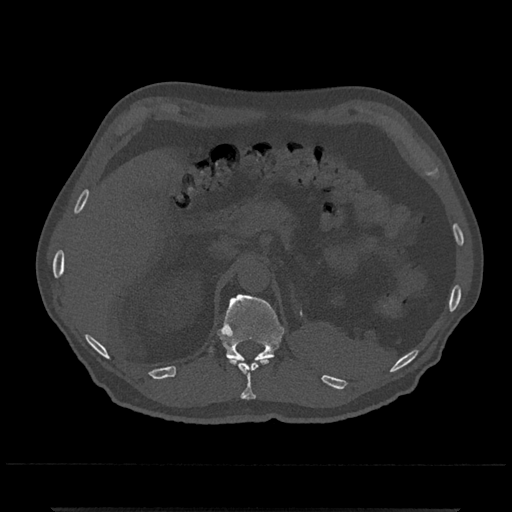
CT including the spine, one axial slice. Slice 452 of 797 in the series (ordered by position). Bone window (W 1800 / L 400 HU). 0.5 mm slice thickness. 512 × 512 image matrix, field of view 393 × 393 mm. Patient: male, 67 years. From the clinical record (not read from this slice): primary cancer: prostate.
Structures marked on this image (semi-automatic segmentation, software-assisted and operator-edited):
- T11 vertebra: bounding box (x1, y1, x2, y2) in pixels: (229, 358, 268, 400)
- T12 vertebra: (217, 294, 284, 363)